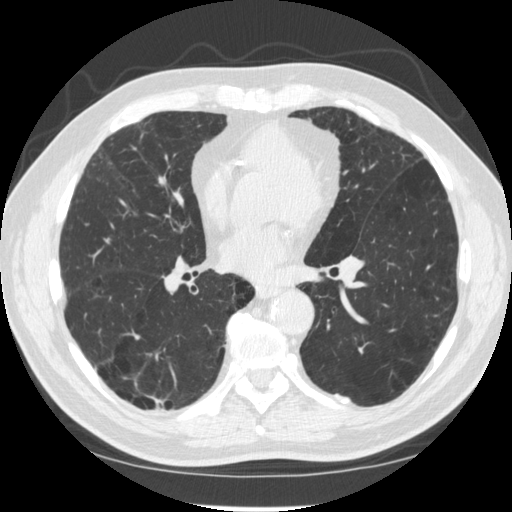
Axial slice from a low-dose chest CT screening exam. Second screening round (one year after baseline). Lung window (W 1500 / L -600 HU). 120 kVp. Slice 149 of 303 in the series. 512 × 512 image matrix. Male participant, aged 70 years at enrolment. Former smoker at enrolment.
- Expert reader's lesion annotation, bounding box (x1, y1, x2, y2) in pixels: (131, 379, 182, 429).
- The screening reader recorded 2 non-calcified nodules or masses ≥4 mm on this exam; which of them this box marks is not recorded.
- Official screen result: negative screen, significant abnormalities not suspicious for lung cancer.
- Later outcome: lung cancer diagnosed 617 days after this screen — squamous cell carcinoma, NOS, right upper lobe, poorly differentiated (G3), stage IV (AJCC 6th edition).